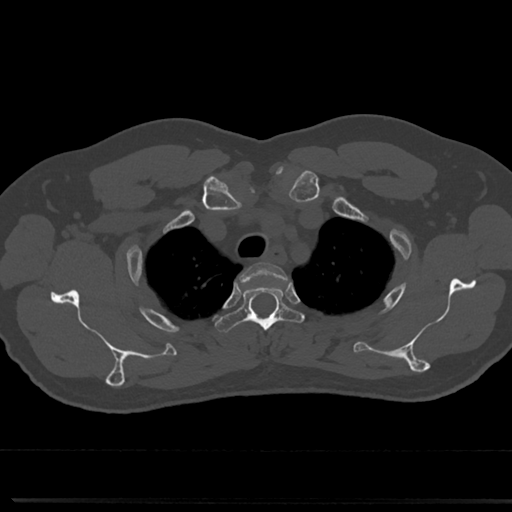
CT including the spine, one axial slice. Slice 602 of 817 in the series (ordered by position). Bone window (W 1800 / L 400 HU). 512 × 512 image matrix, field of view 355 × 355 mm. Male patient, age 61 years. Case-level facts recorded for this patient, not image findings: primary cancer: prostate.
Outlined on this slice (semi-automatic segmentation, software-assisted and operator-edited):
- T2 vertebra: bounding box <245,263,284,279> (left, top, right, bottom; pixels)
- T3 vertebra: <218,280,299,337>